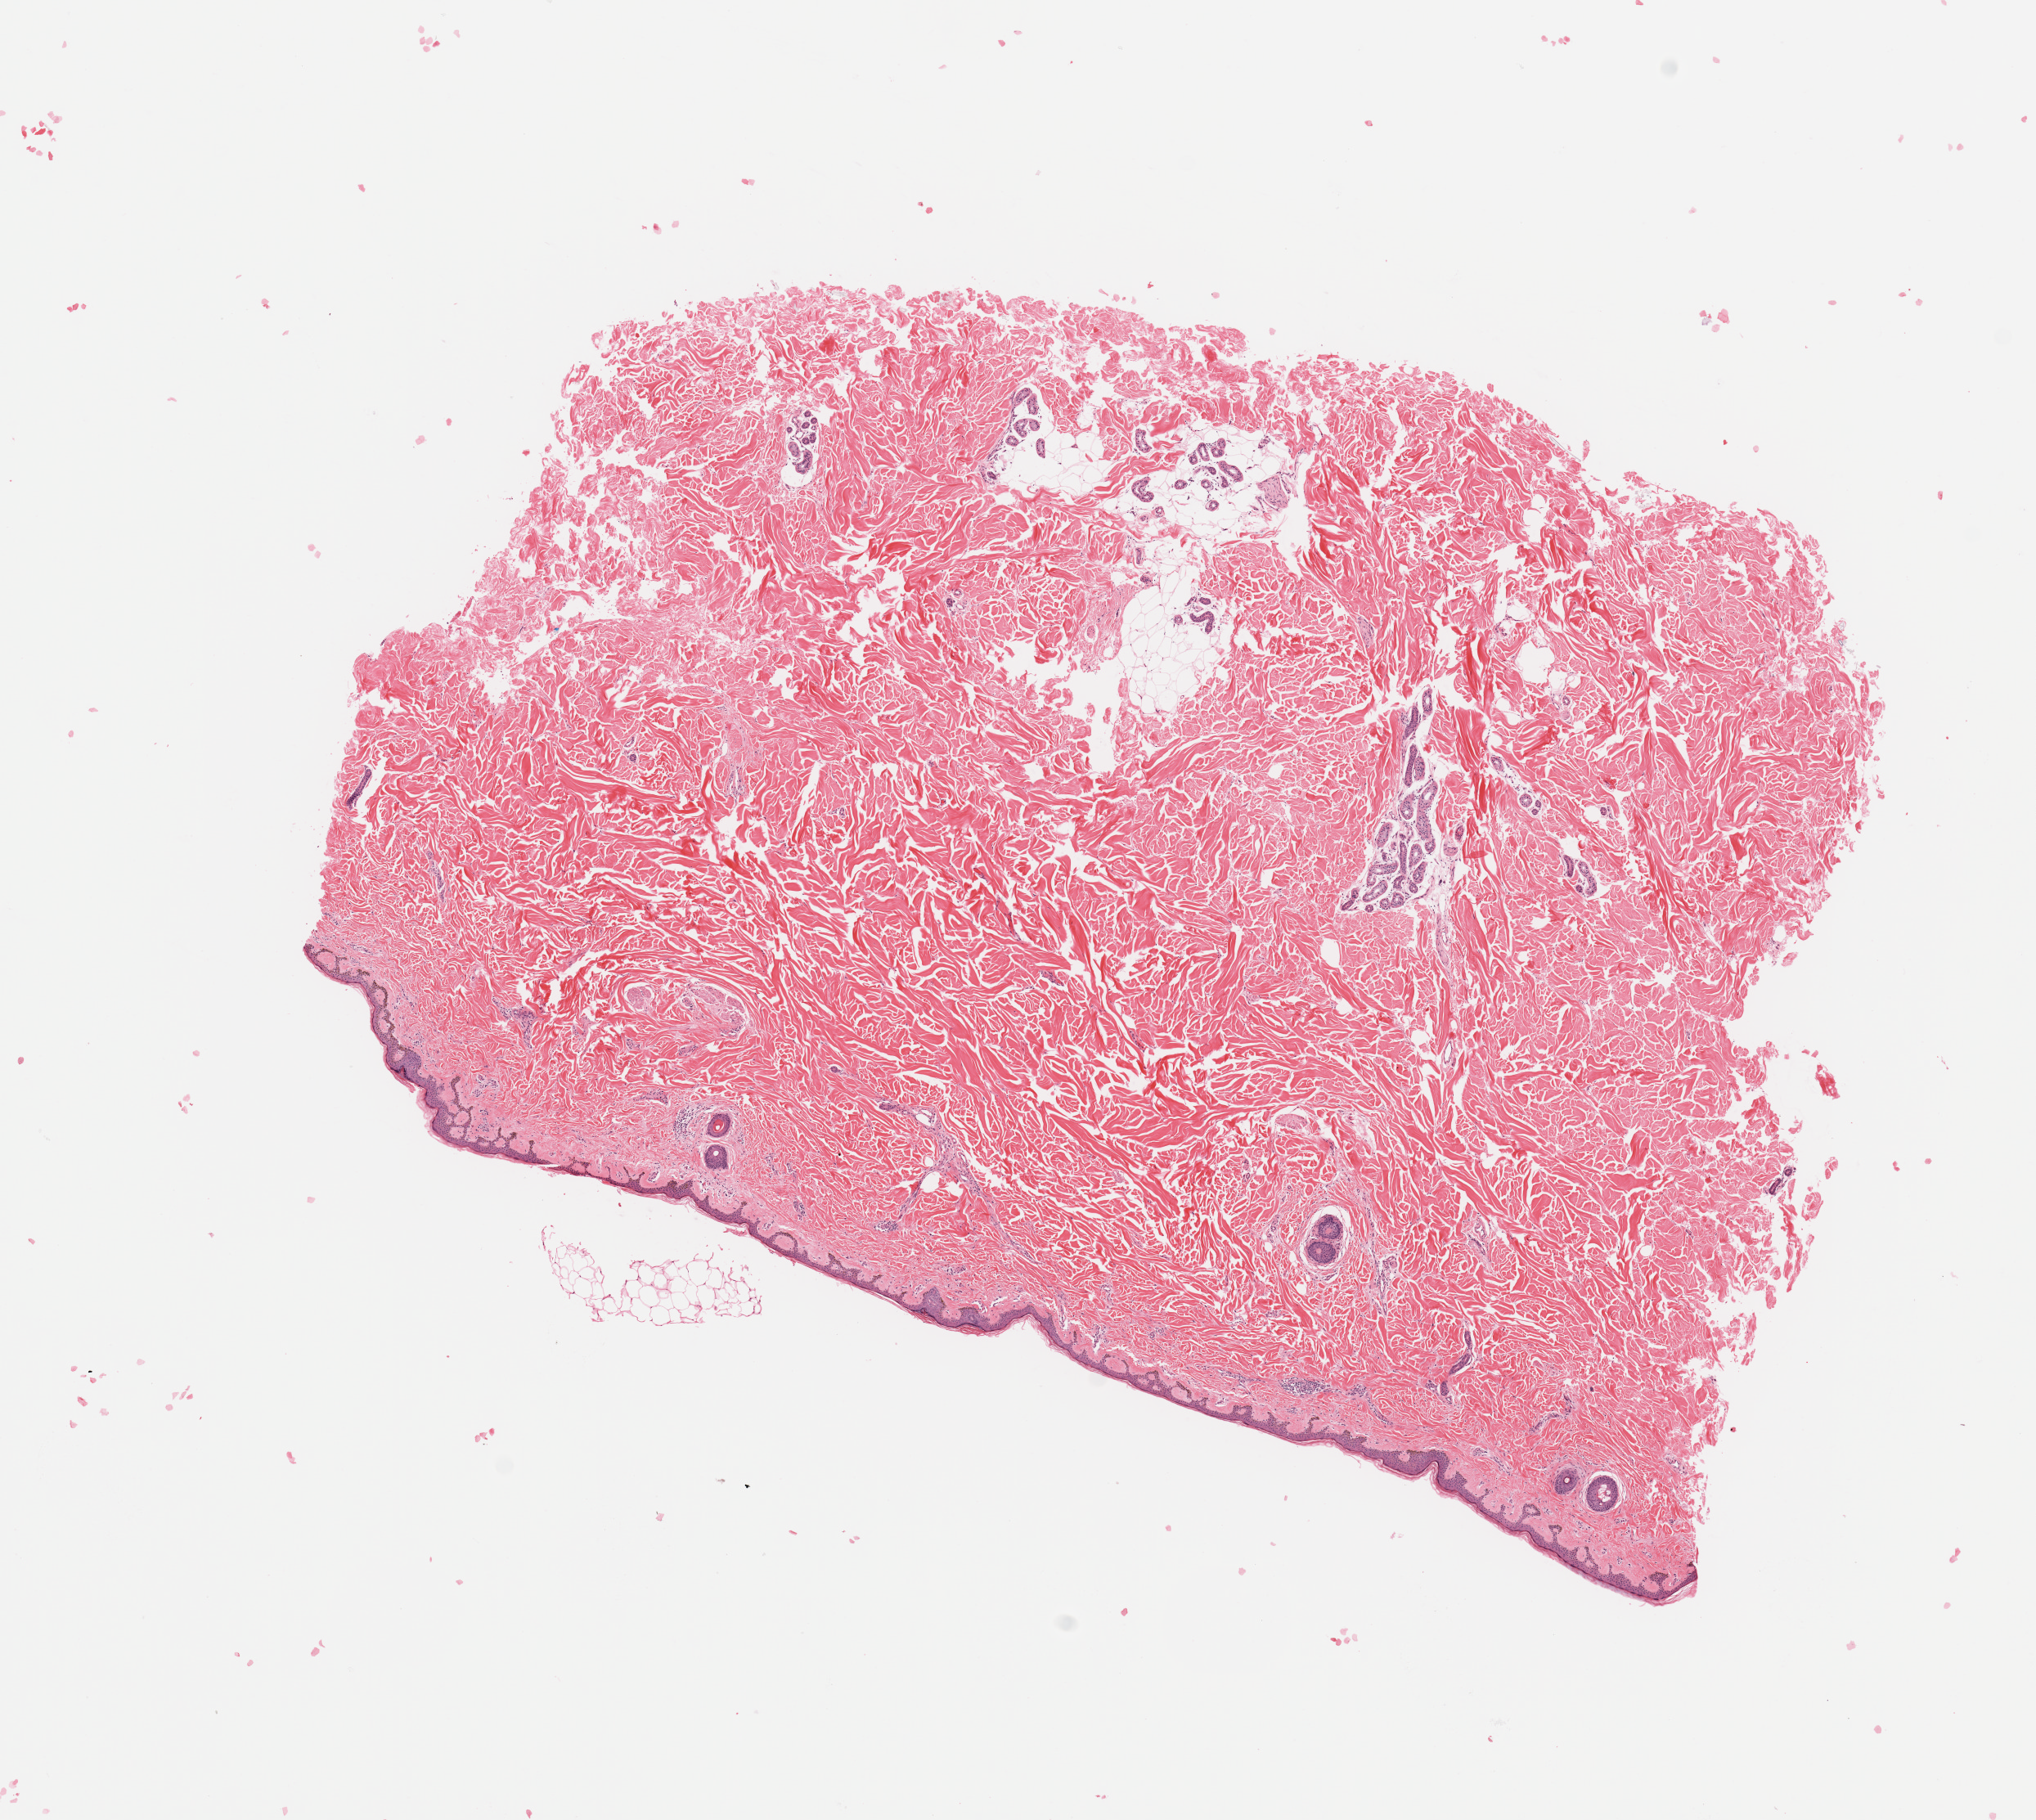
Digitized H&E-stained tissue section (whole slide), a low-resolution overview of the entire scanned area, about 9.8 x 8.8 mm (from a 20x scan); normal (non-tumour) tissue (melanoma cohort); sampled site not recorded. Patient: female, age 66 years.
This section: normal (non-tumour) tissue from the same patient. Patient diagnosis (cohort enrolment): cutaneous melanoma (skin).